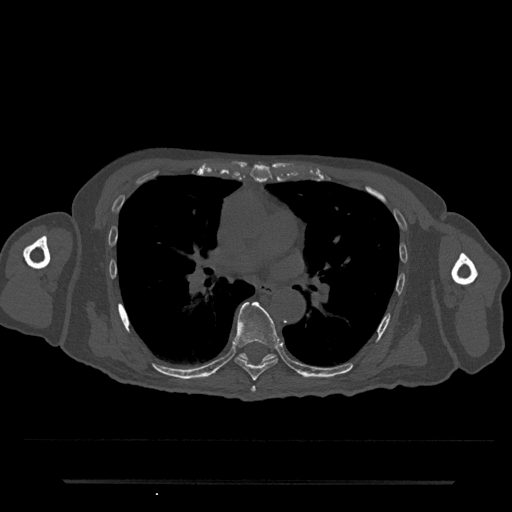
CT including the spine, one axial slice; slice 466 of 797 in the series (ordered by position); reconstruction kernel Br40s/3; bone window (W 1800 / L 400 HU); 512 × 512 image matrix, field of view 427 × 427 mm. Male patient, age 74 years. Case-level facts recorded for this patient, not image findings: primary cancer: prostate.
Outlined on this slice (semi-automatically segmented with operator editing):
- T6 vertebra: box from (x=251, y=386) to (x=256, y=392) px
- T7 vertebra: (x=234, y=302)–(x=280, y=381)
- T8 vertebra: (x=239, y=353)–(x=276, y=362)